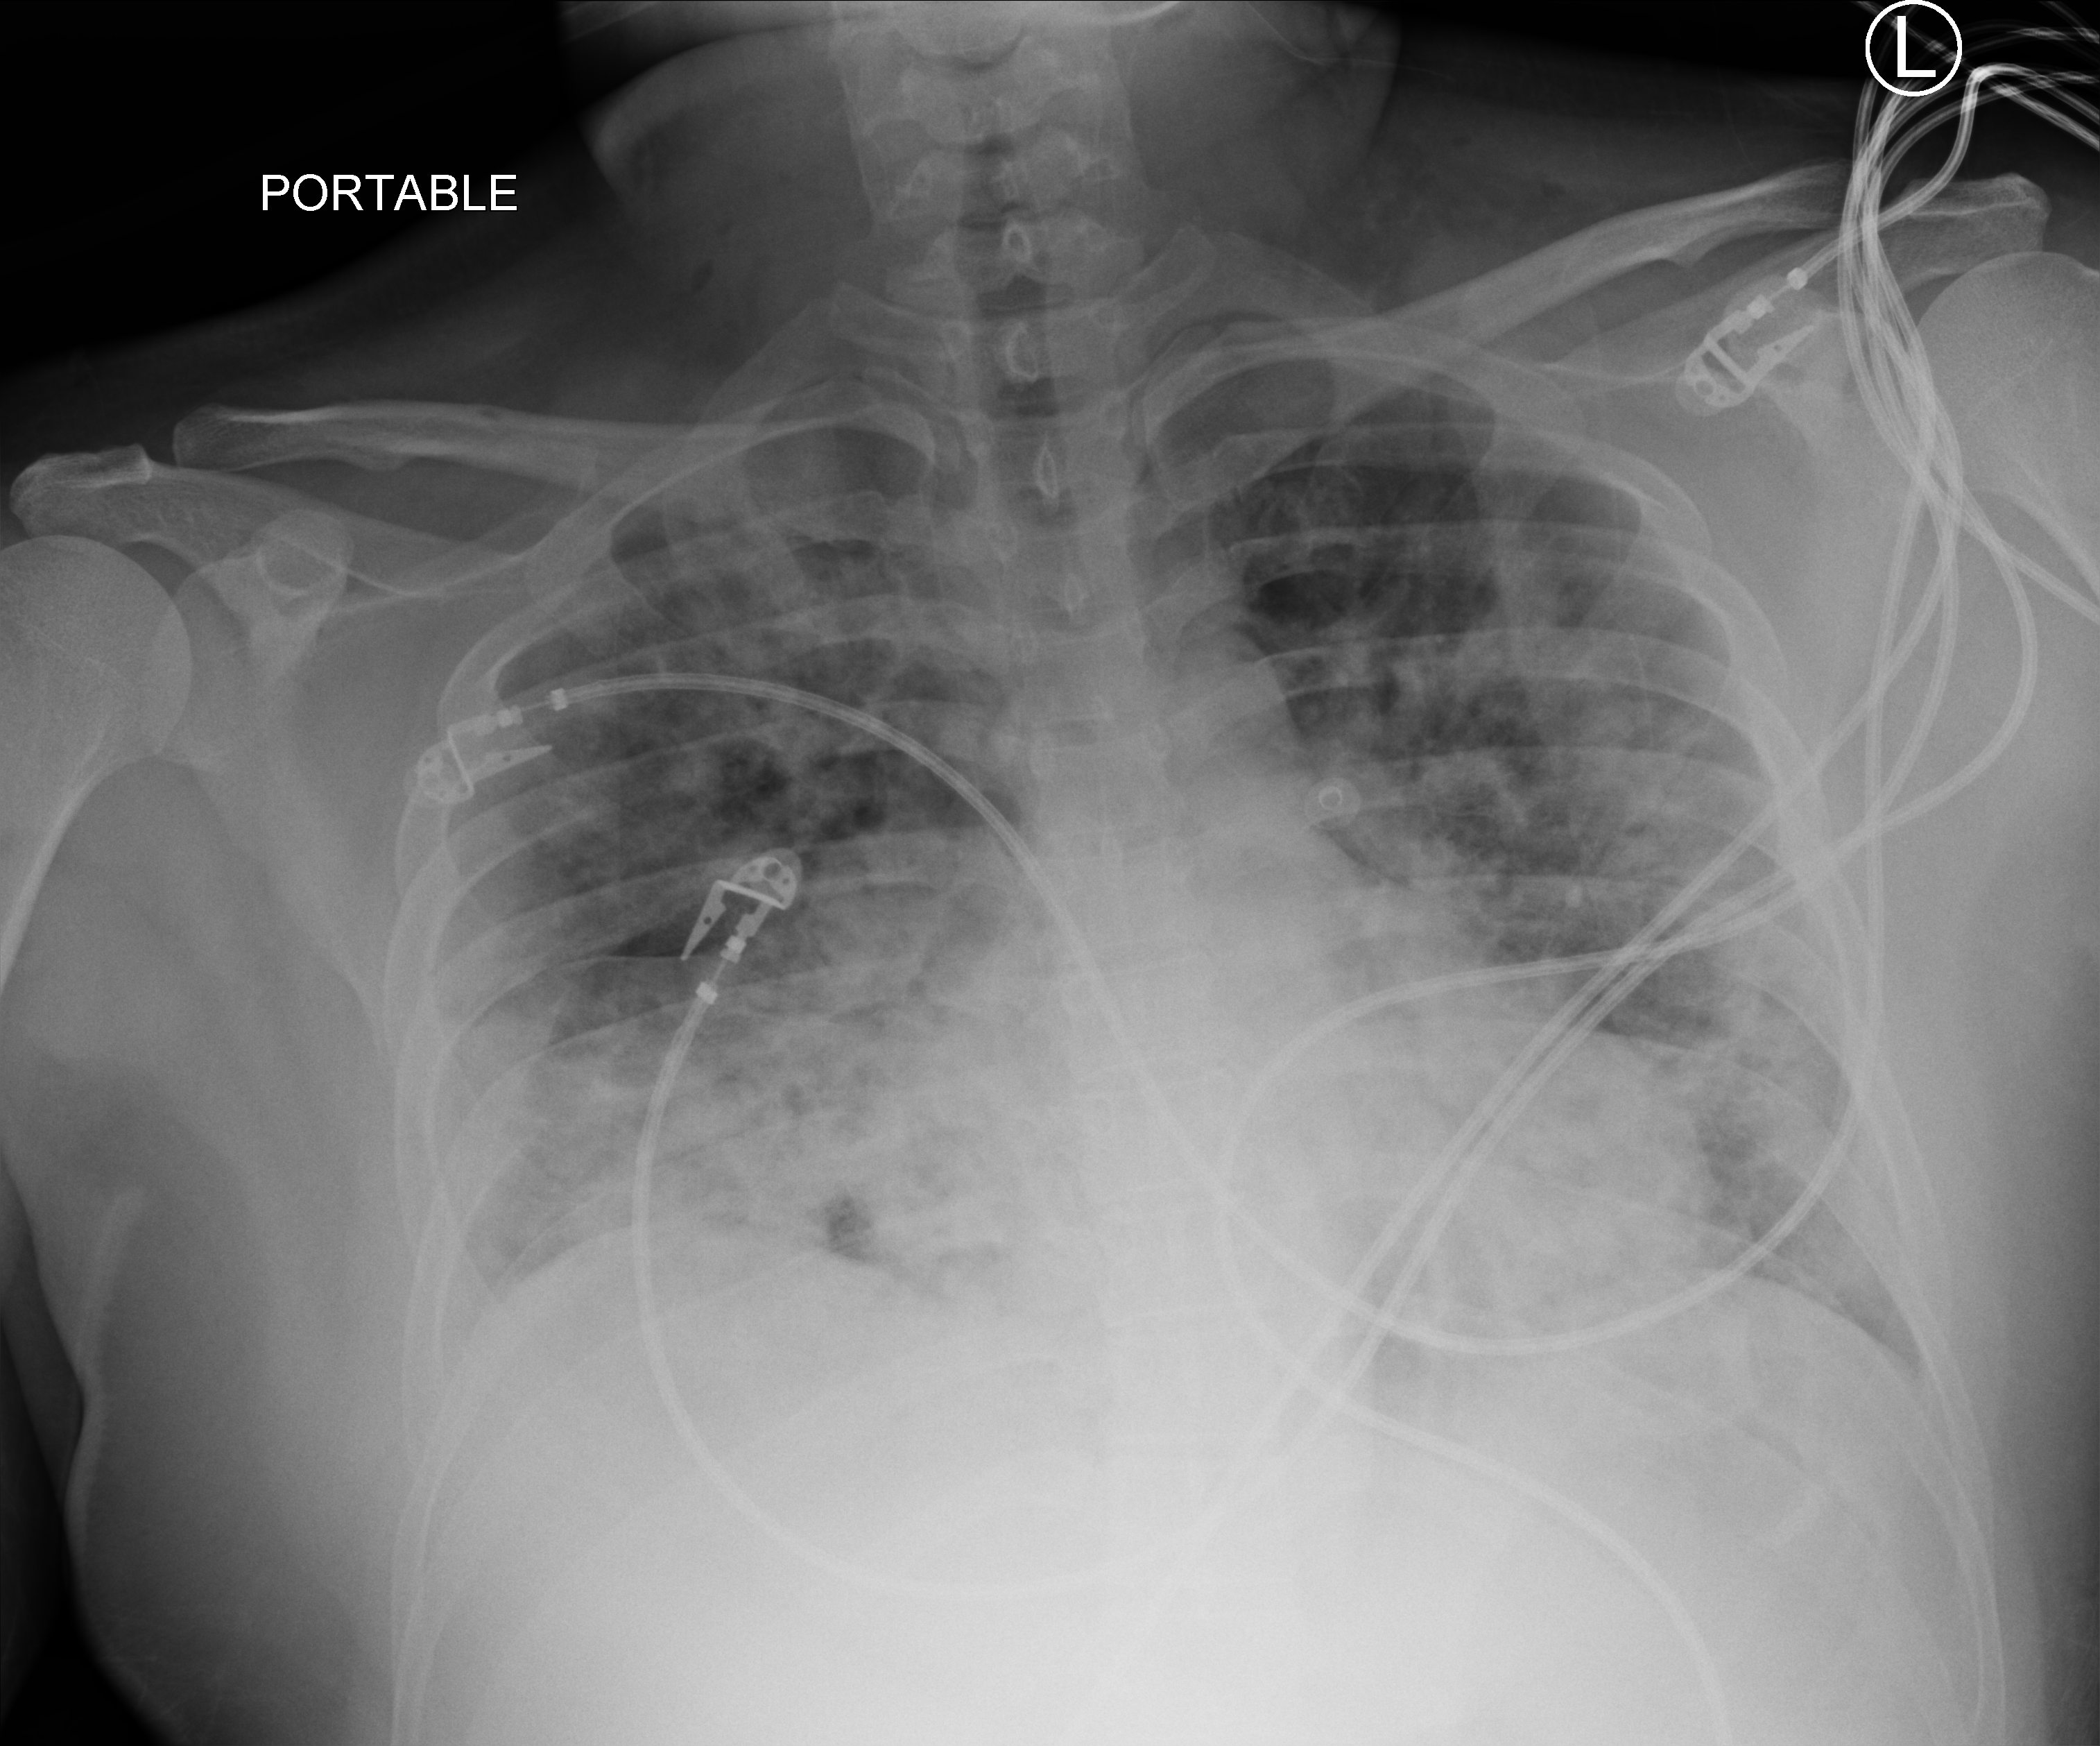
Bedside chest radiograph (computed radiography). Patient hospitalised with COVID-19; male, aged 18–59 years.
Hospital-stay facts (about this admission, not read from this image; timing relative to this image not recorded): diabetes (admission record): no.